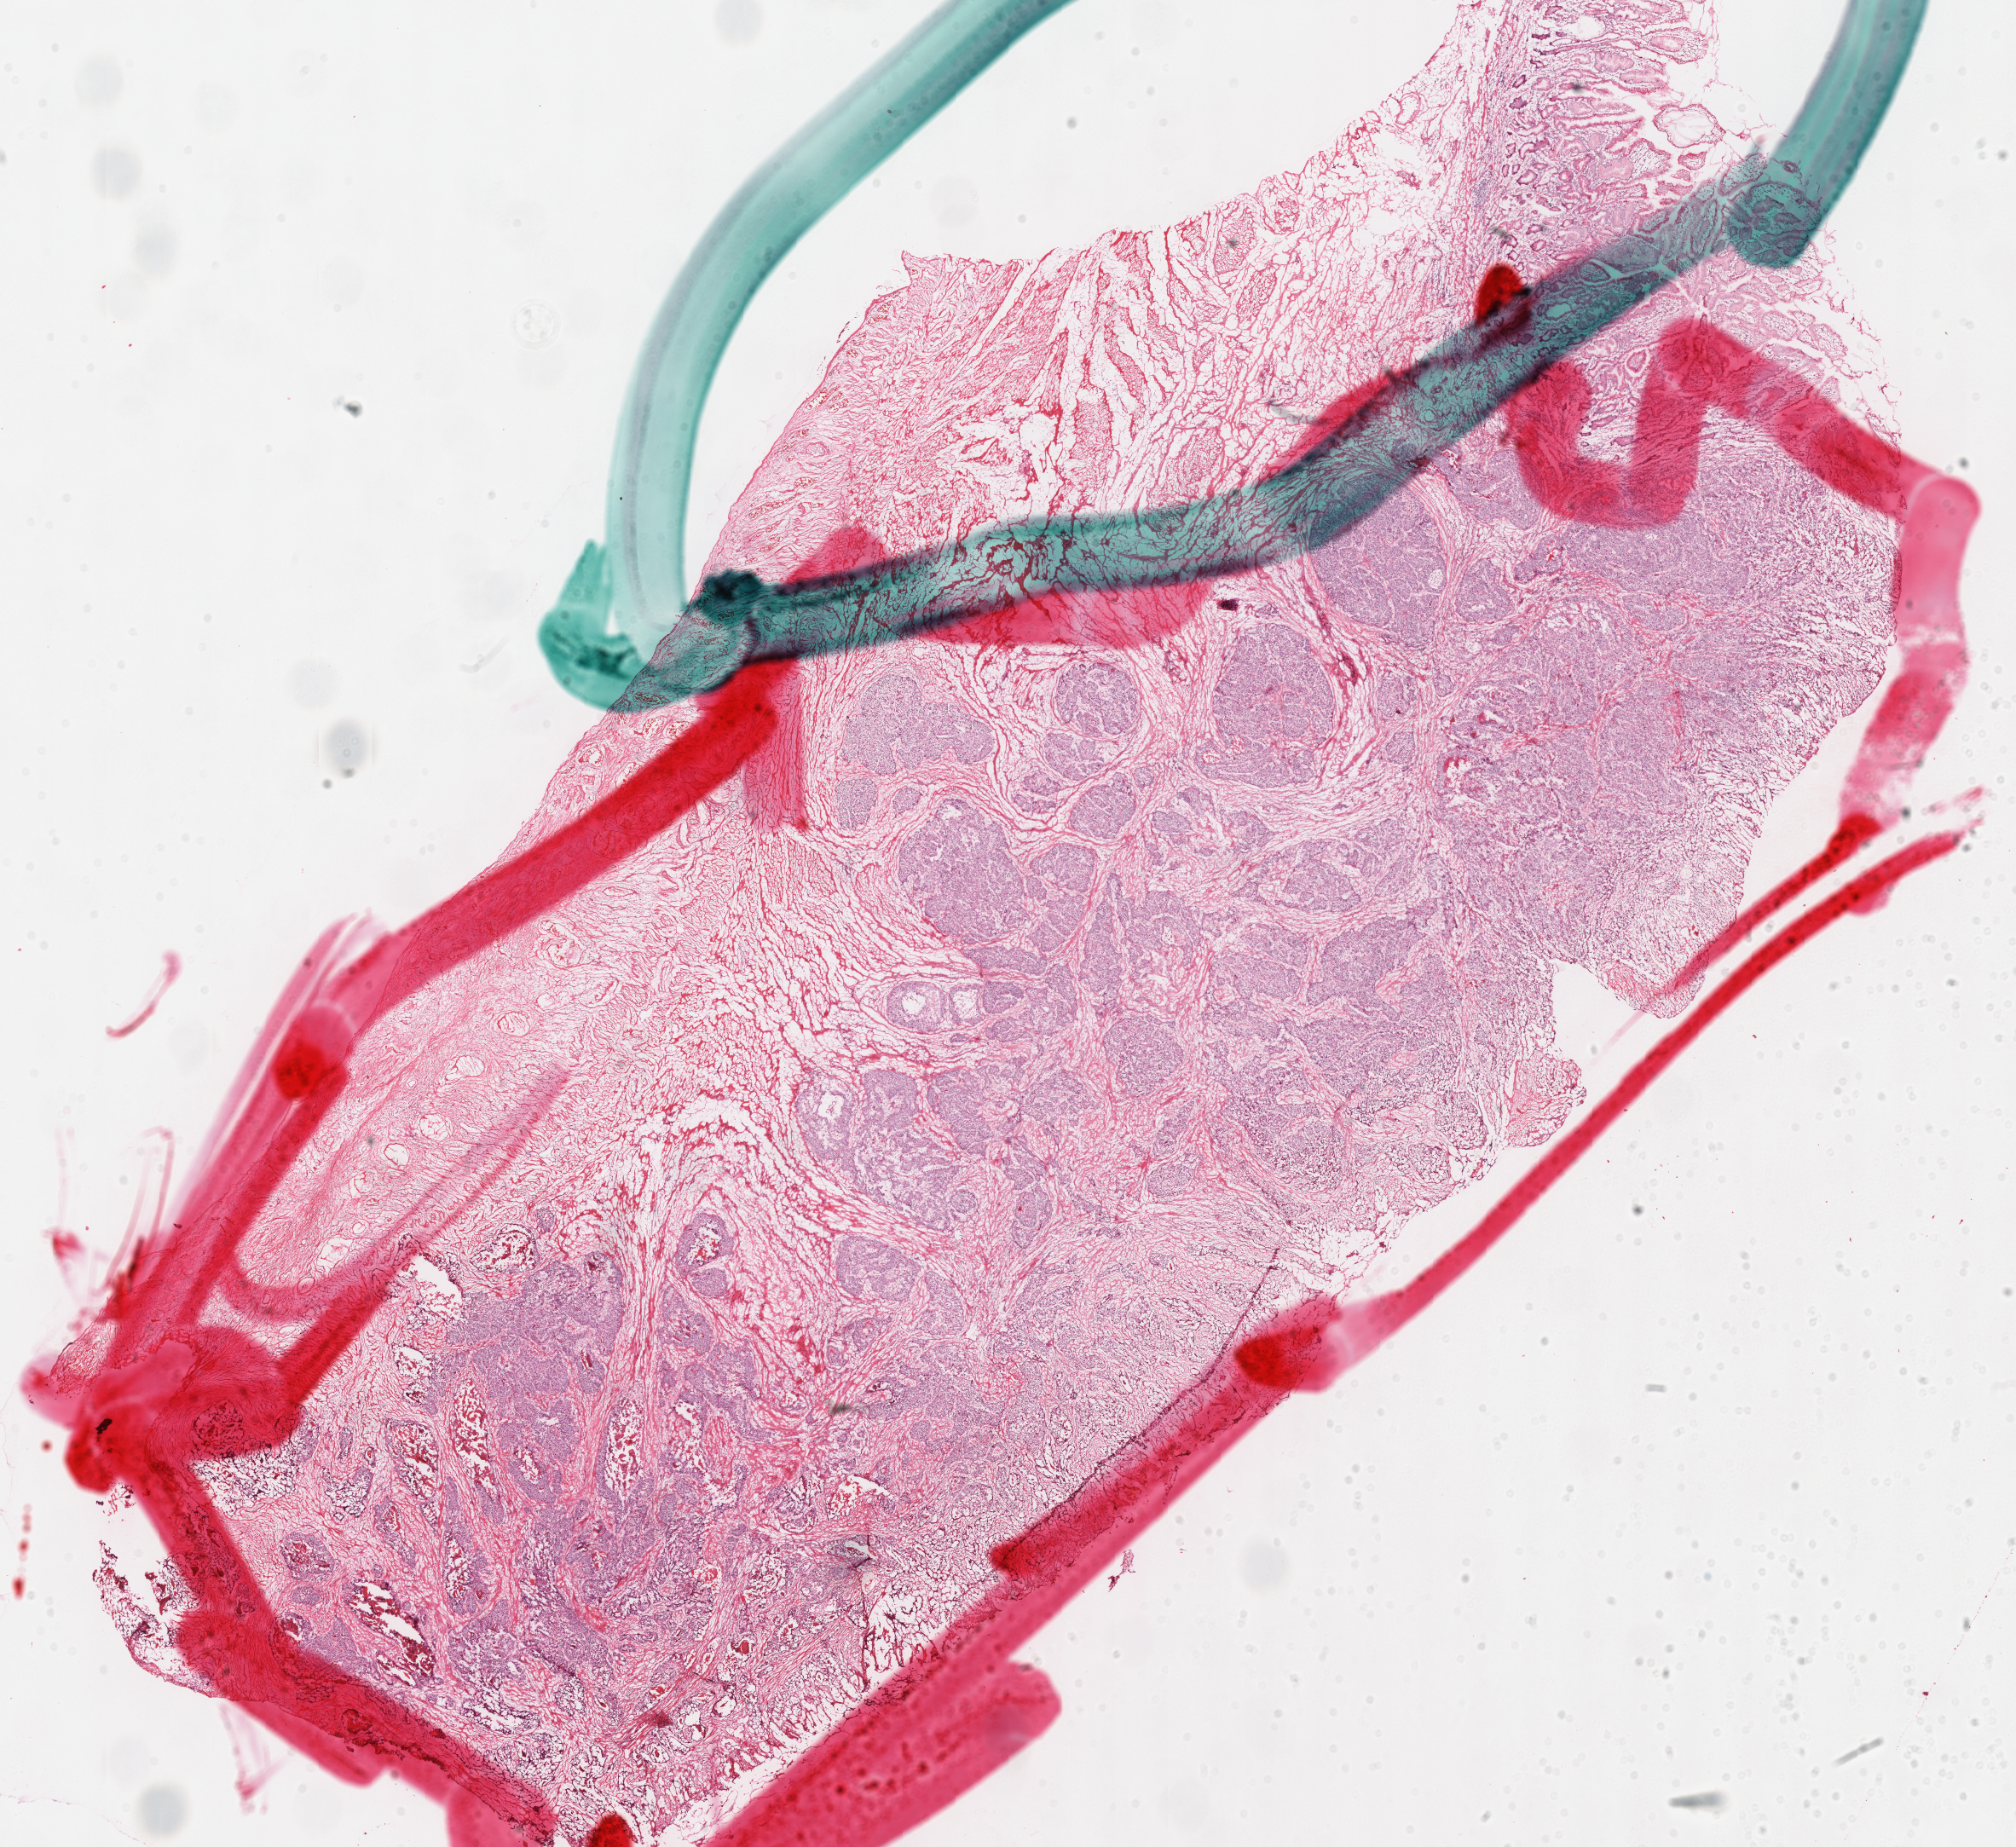
Whole-slide histology image, H&E-stained — a low-resolution overview of the entire scanned area, about 18.6 x 17.0 mm (from a 40x scan), frozen section, primary tumour sample from the stomach. Male, age 65 years at initial diagnosis. Histologic grade: G2 (moderately differentiated). Slide review estimates, as recorded: tumour cells 90%, tumour nuclei 75%, normal cells 5%, necrosis 5%. Inflammatory infiltration, as recorded: lymphocyte infiltration 5%, monocyte infiltration 0%, neutrophil infiltration 0%.
• lymph nodes positive (case pathology): 0 of 9 examined
• AJCC pathologic stage: IIA
• diagnosis: Adenocarcinoma, NOS
• TNM: T3 N0 M0